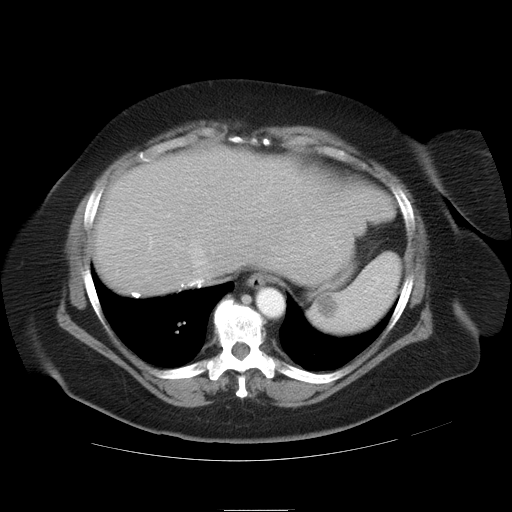
Contrast-enhanced abdominal CT, one axial slice; slice 31 of 37 in the series (ordered by position); reconstruction kernel STANDARD; 120 kVp; soft-tissue window (W 400 / L 40 HU); 512 × 512 image matrix, field of view 422 × 422 mm. Female patient, age 68 years. Case-level facts recorded for this patient, not image findings: diagnosis: colorectal cancer liver metastases, imaged before liver resection; multiple liver metastases: no; largest metastasis: 2 cm; disease in both lobes: no.
Outlined on this slice (manually delineated by an expert):
- hepatic veins: bounding box <188,232,207,268> (left, top, right, bottom; pixels)
- liver: <95,149,396,298>
- planned liver remnant (the part of the liver to remain after resection): <95,148,396,298>
- portal vein (with intrahepatic branches): <150,240,152,245>